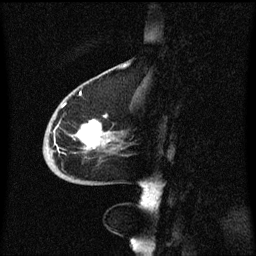
Breast MRI (dynamic contrast-enhanced), one sagittal slice. Position 21 of 60 along the scan axis. Dynamic contrast-enhanced series, image 2 of 3 at this slice position (ordered by acquisition). 1.5 T. TE 4.2 ms, TR 8.4 ms. 2 mm slice thickness. 256 × 256 image matrix. Female patient, age 68 years. From the clinical record (not read from this slice): setting: breast cancer imaged before/during neoadjuvant chemotherapy; receptor status: triple-negative.
Structures marked on this image (semi-automatically segmented with operator editing):
- analysis volume of interest (the breast-tissue region the enhancement analysis was run in; not a lesion): box from (x=44, y=94) to (x=127, y=173) px
- tumour enhancement mask (voxels above the 70 % enhancement threshold inside the analysis volume of interest): (x=77, y=96)–(x=112, y=151)